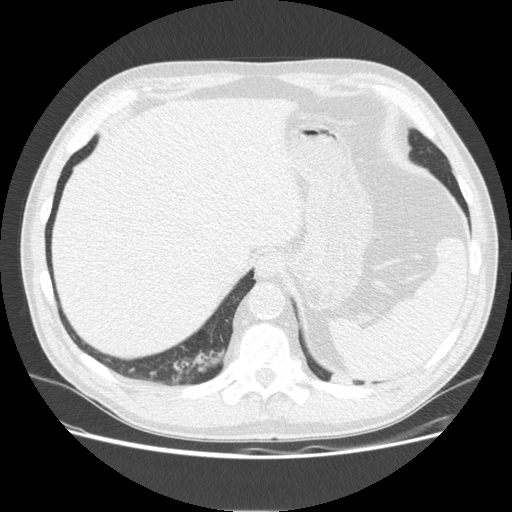
Low-dose screening chest CT, one axial slice; slice 36 of 165 in the series (ordered by position); lung window (W 1500 / L -600 HU); 512 × 512 image matrix, field of view 375 × 375 mm.
Structures marked on this image (outlined manually by an expert reader):
- lesion 1 (tumor, upper lobe of left lung): bounding box [x1, y1, x2, y2] px = [330, 375, 353, 384]